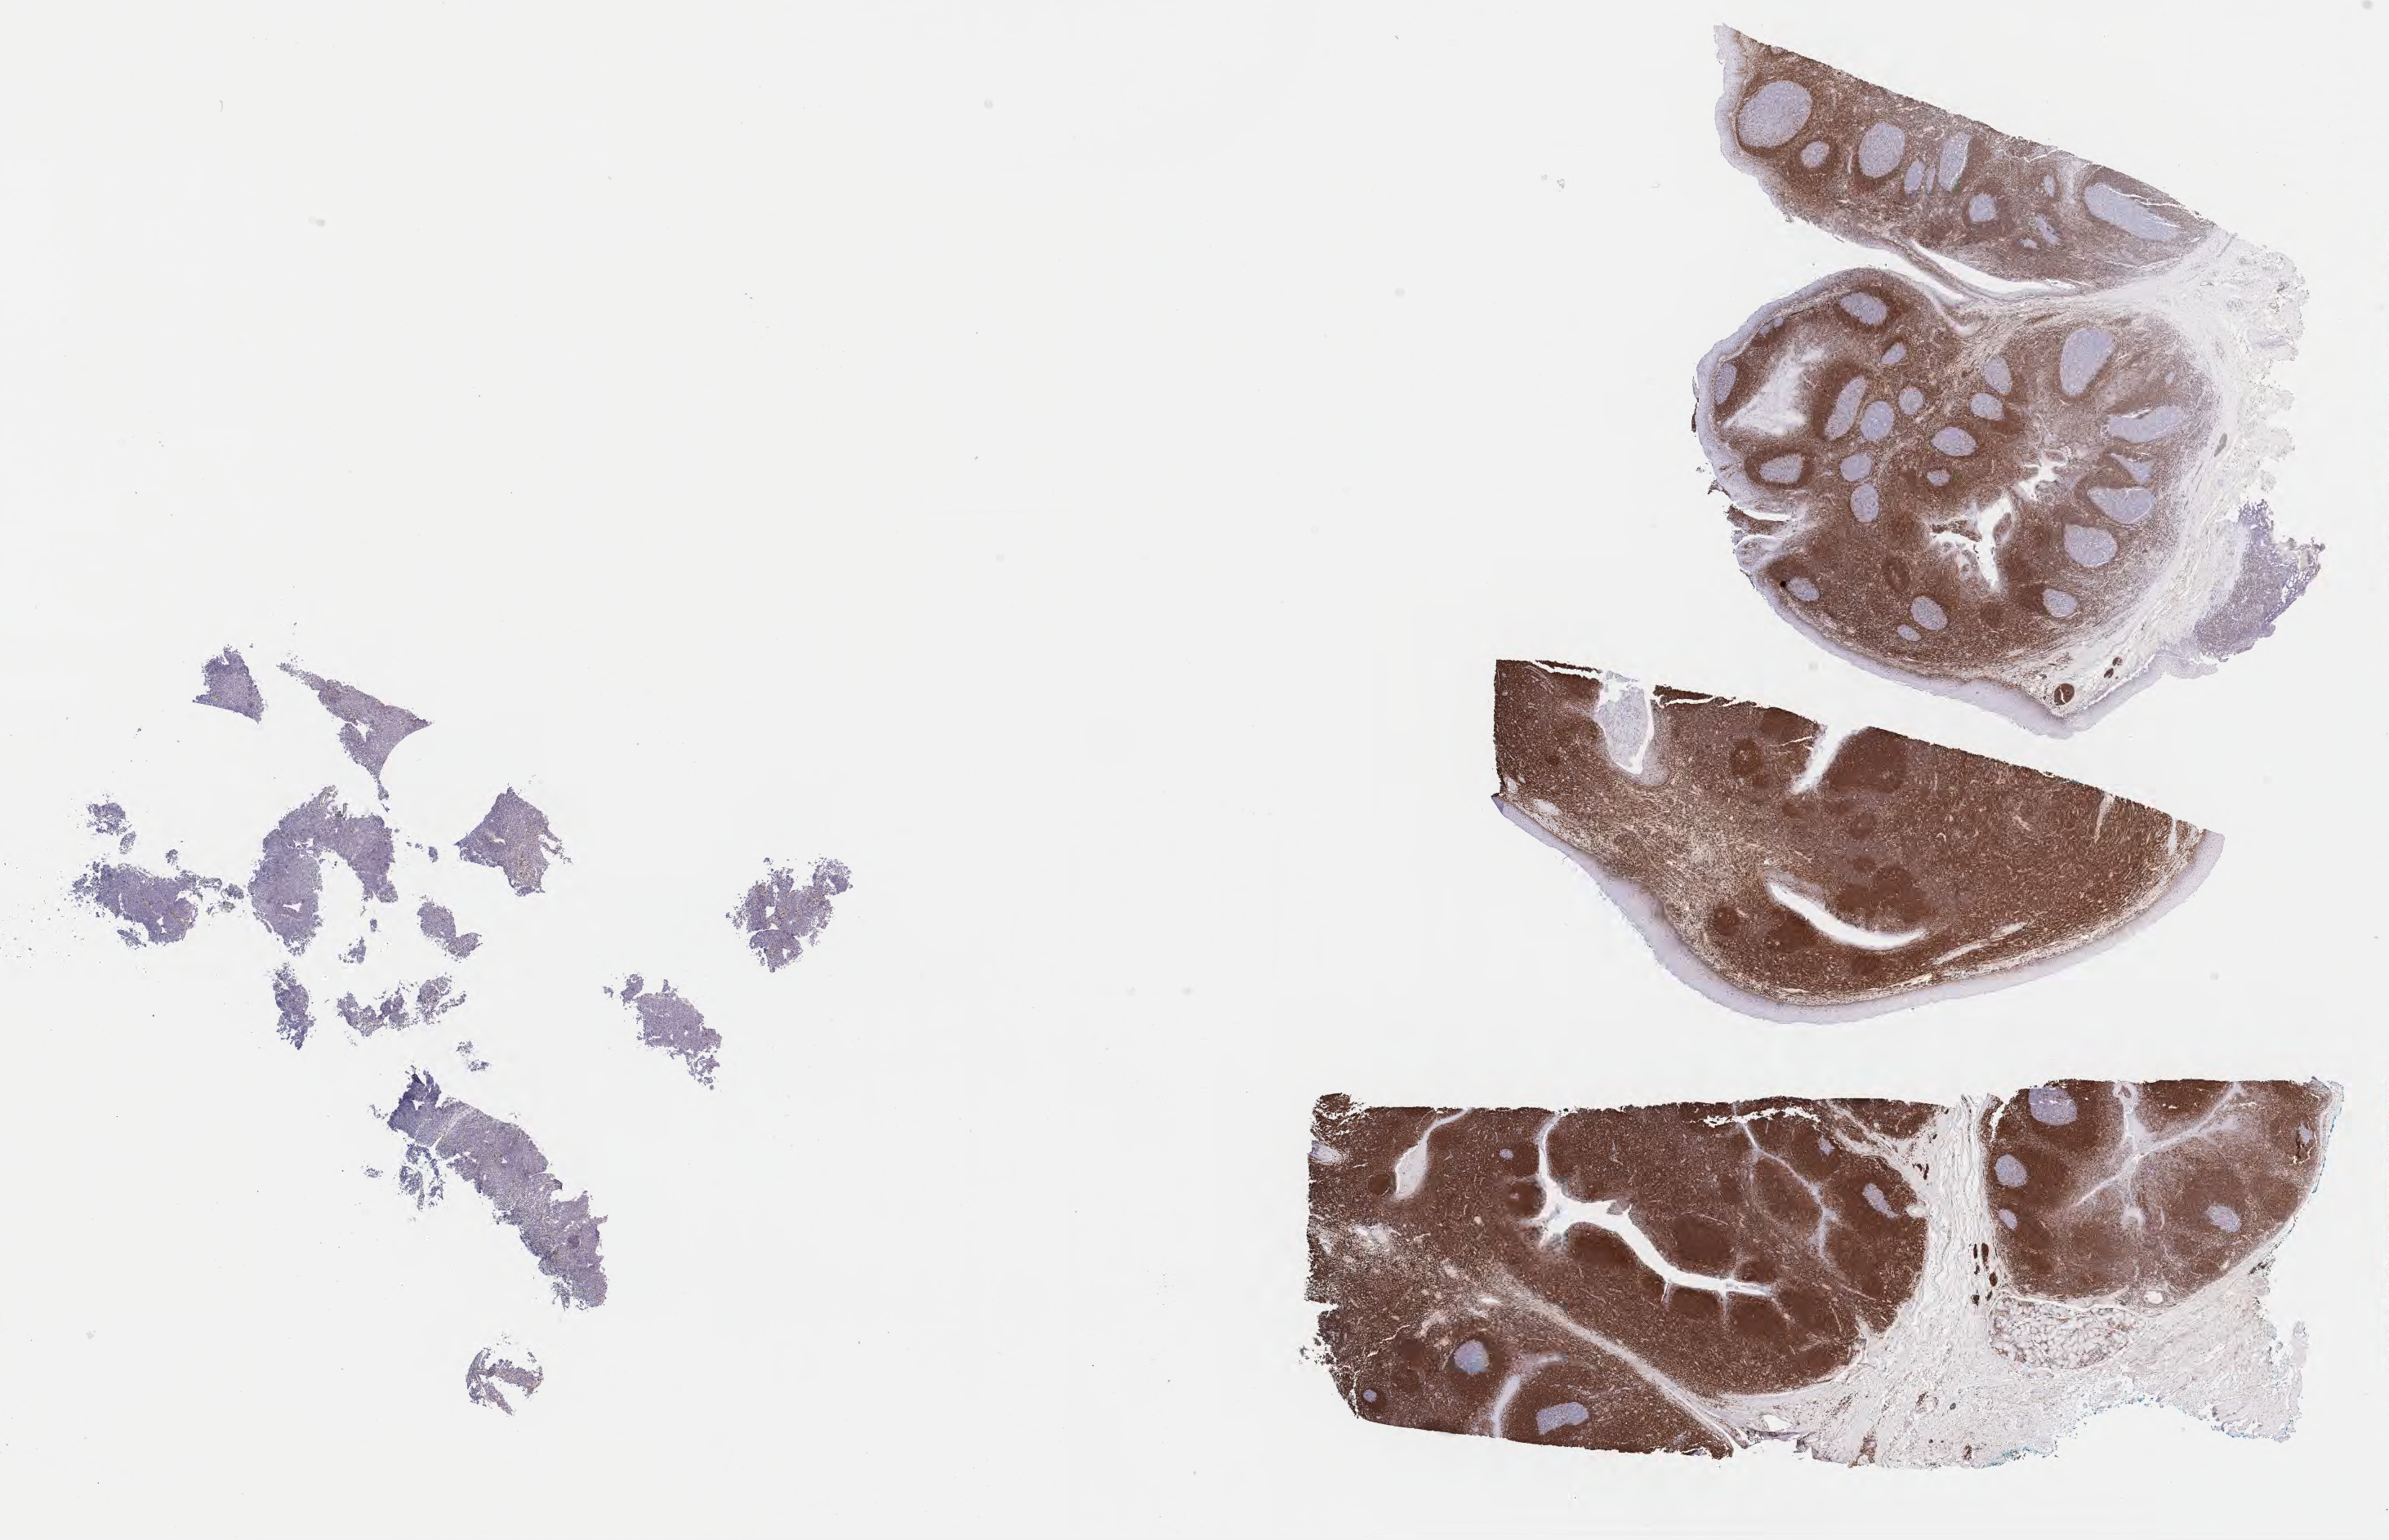
Whole-slide image, immunohistochemical stain for BCL2, shown as a low-resolution overview of the whole scanned area (about 23.7 x 15.3 mm). Tumor tissue. Site: kidney. Female patient; age at initial diagnosis 8 years.
• histologic diagnosis: Burkitt lymphoma, NOS